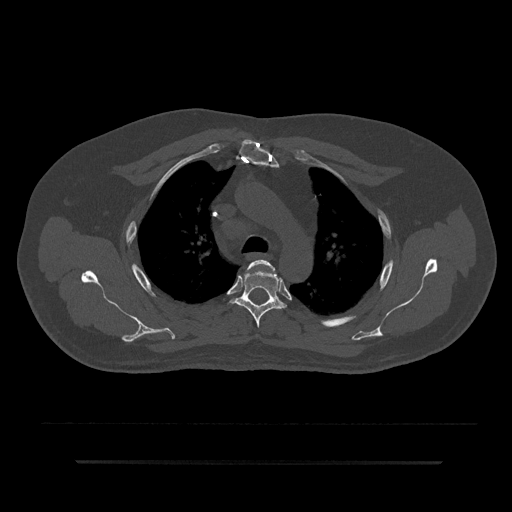
CT including the spine, one axial slice; position 620 of 797 along the scan axis; reconstruction kernel Br40s/3; bone window (W 1800 / L 400 HU); 0.5 mm slice thickness; 512 × 512 image matrix. Male patient, age 59 years. From the clinical record (not read from this slice): primary cancer: bile ducts.
Outlined on this slice (semi-automatically segmented with operator editing):
- T3 vertebra: bounding box [x1, y1, x2, y2] px = [247, 260, 276, 274]
- T4 vertebra: [230, 268, 286, 328]